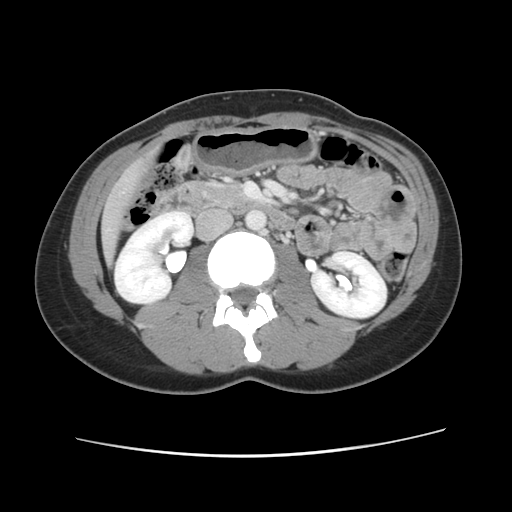
Contrast-enhanced abdominal CT, one axial slice. Slice 26 of 134 in the series (ordered by position). Intravenous contrast given. Soft-tissue window (W 400 / L 40 HU). 2.5 mm slice thickness. 512 × 512 image matrix, field of view 339 × 339 mm. Female patient, age 33 years. Case-level facts recorded for this patient, not image findings: diagnosis: colorectal cancer liver metastases, imaged before liver resection; multiple liver metastases: yes; largest metastasis: 4.5 cm; disease in both lobes: yes.
Outlined on this slice (manually delineated by an expert):
- liver: box from (x=101, y=156) to (x=153, y=262) px
- planned liver remnant (the part of the liver to remain after resection): (x=104, y=246)–(x=113, y=263)